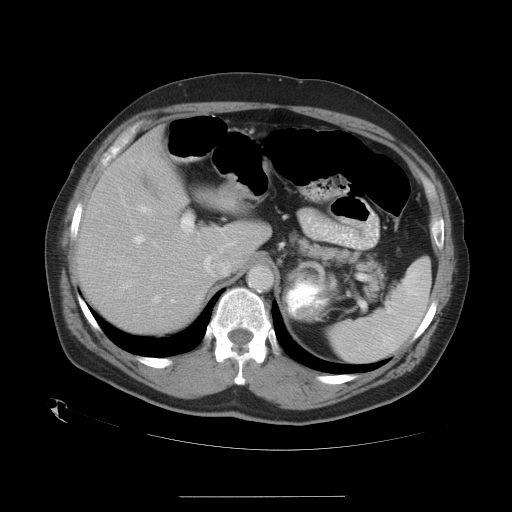
Contrast-enhanced abdominal CT, one axial slice; position 22 of 35 along the scan axis; reconstruction kernel STANDARD; 120 kVp; intravenous contrast given; soft-tissue window (W 400 / L 40 HU); 7.5 mm slice thickness; 512 × 512 image matrix, field of view 450 × 450 mm. Male patient, age 67 years. From the clinical record (not read from this slice): diagnosis: colorectal cancer liver metastases, imaged before liver resection; multiple liver metastases: no; largest metastasis: 2.3 cm; disease in both lobes: no.
Annotated regions visible in this slice (outlined manually by an expert reader):
- hepatic veins: bounding box <140,206,159,301> (left, top, right, bottom; pixels)
- liver: <78,131,266,334>
- planned liver remnant (the part of the liver to remain after resection): <86,131,266,334>
- portal vein (with intrahepatic branches): <124,215,209,288>